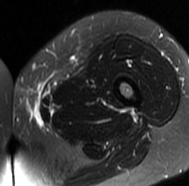
MRI of an extremity soft-tissue mass, one axial slice. Slice 18 of 77 in the series (ordered by position). T2-weighted fat-saturated. MR volume resampled by the dataset authors to the PET/CT grid (not the native acquisition matrix). 3.27 mm slice thickness. 189 × 186 image matrix. Female patient. From the clinical record (not read from this slice): histological type: leiomyosarcoma; grade: high; site of the primary tumour: groin.
Outlined on this slice (expert contour drawn on MRI and transferred to this co-registered scan by the dataset authors):
- gross tumour volume including surrounding oedema: bounding box [x1, y1, x2, y2] px = [13, 91, 43, 124]